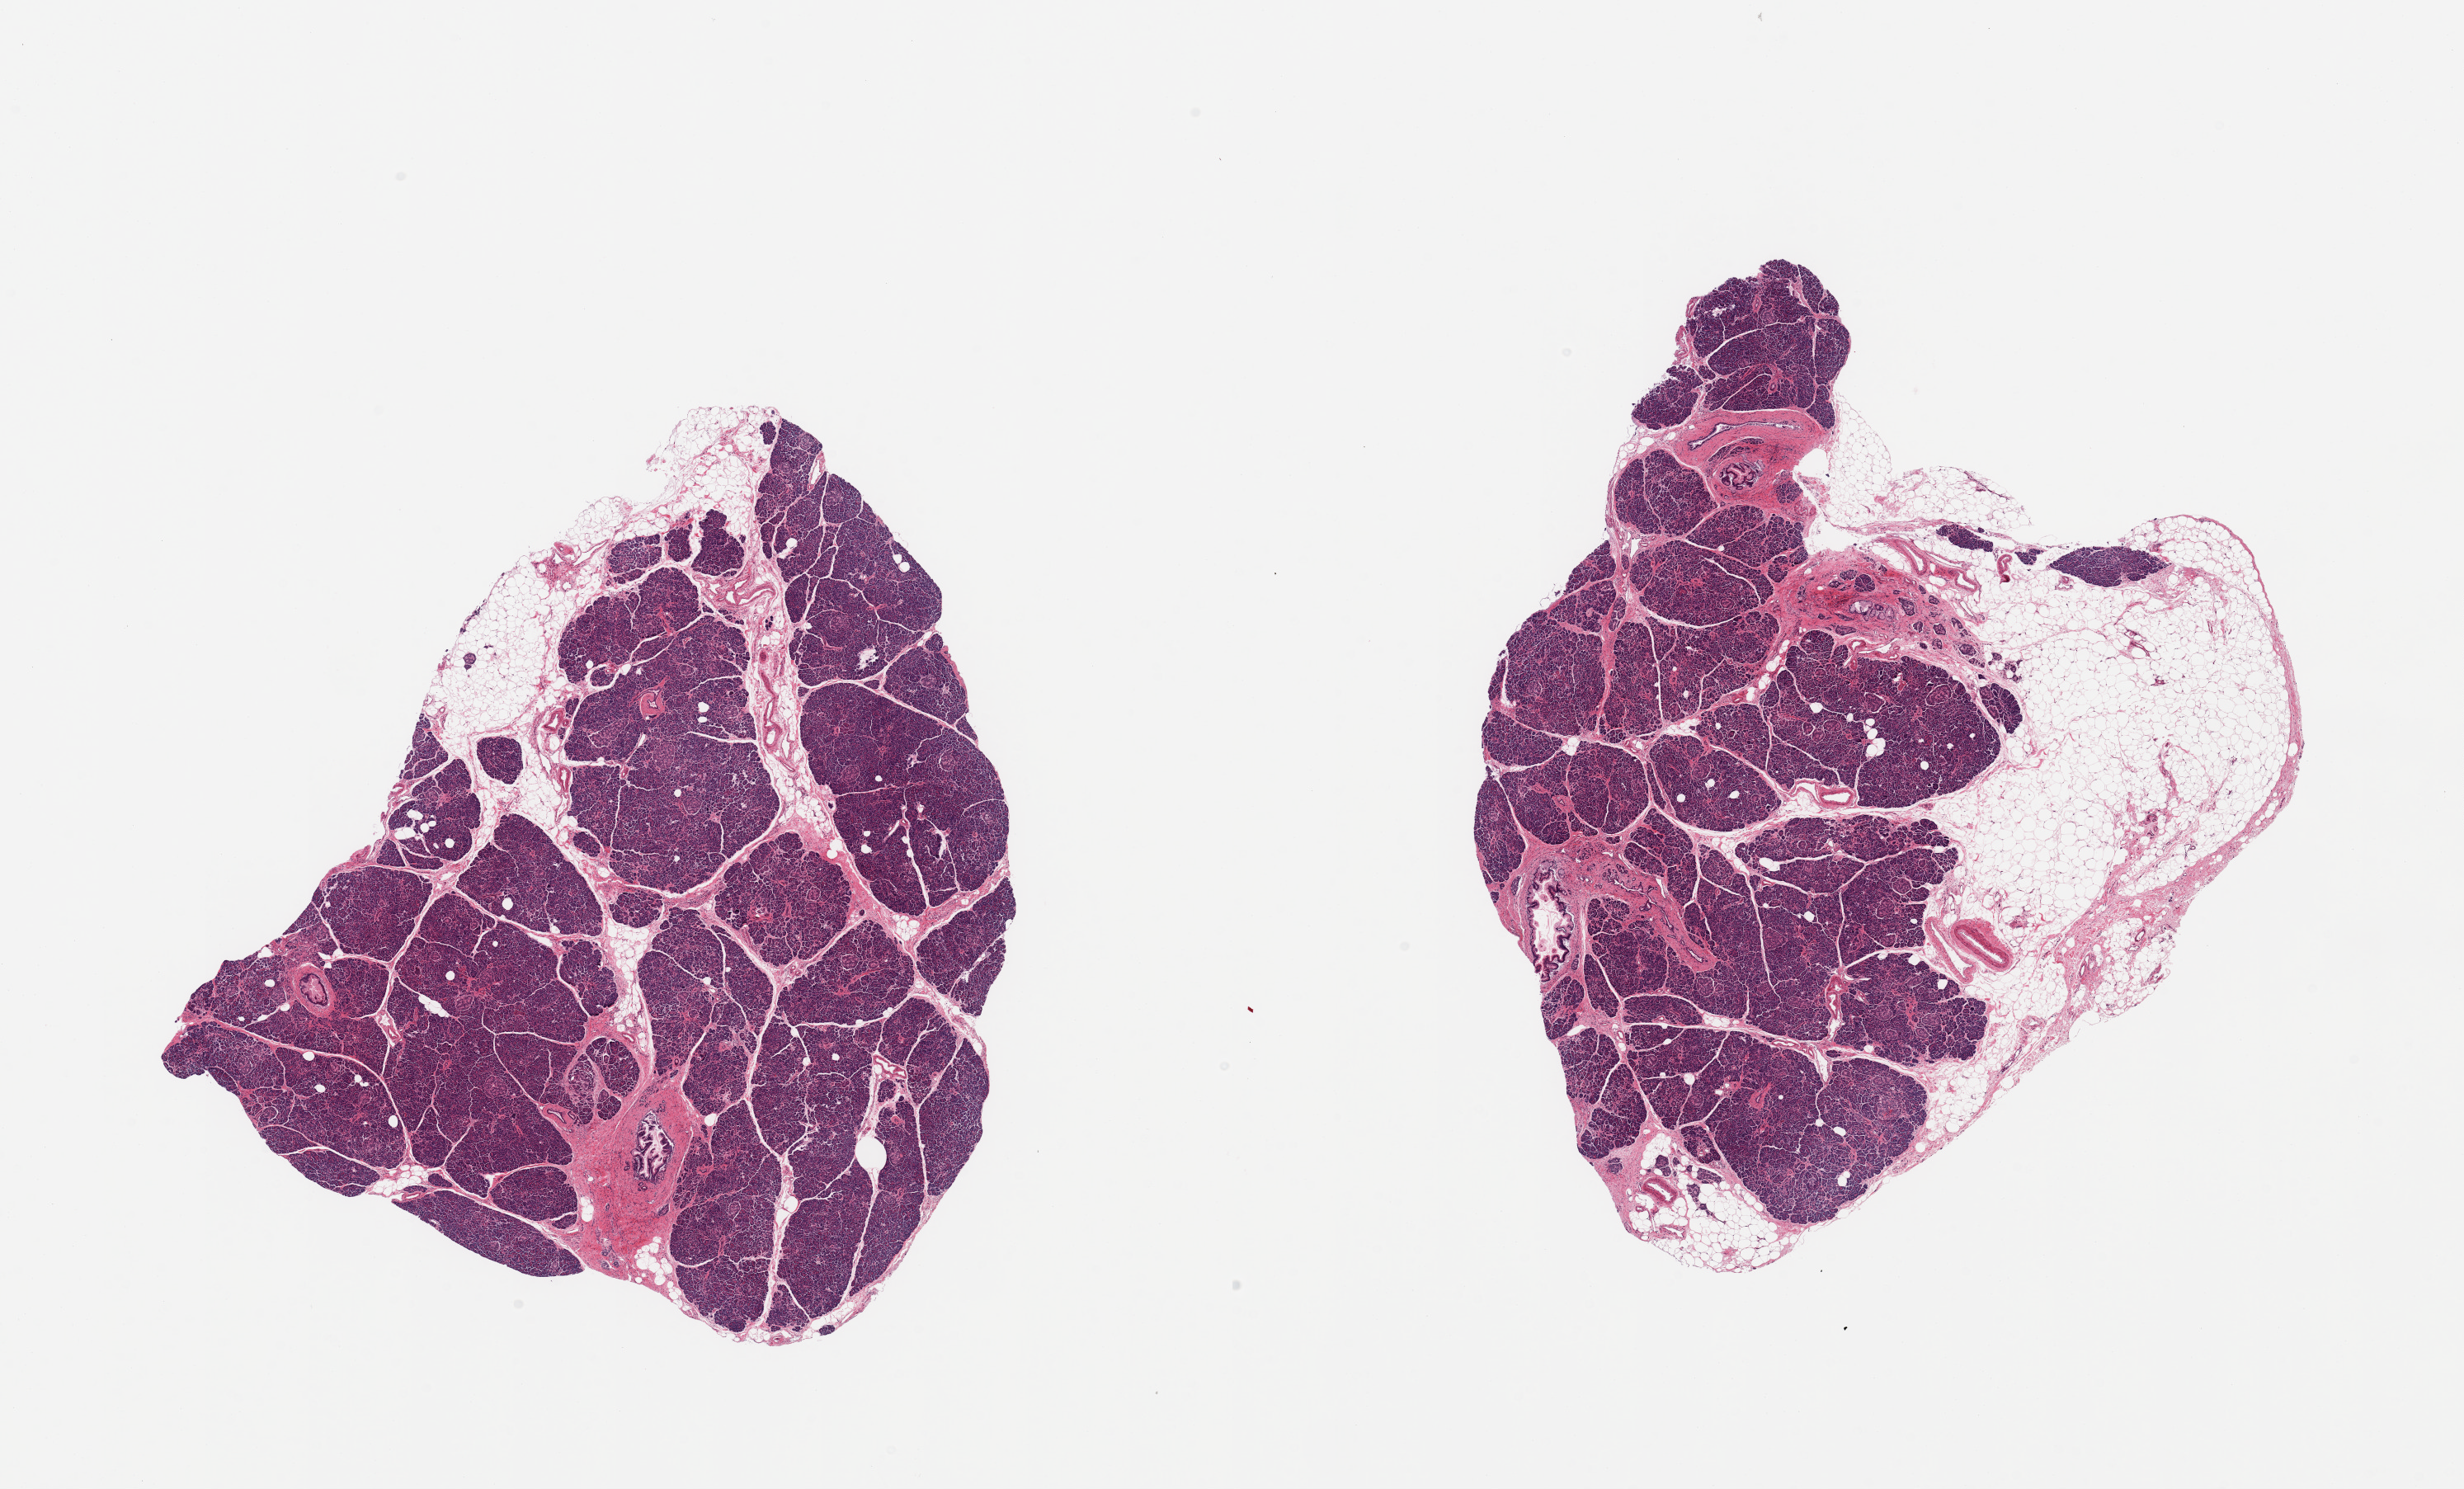
Haematoxylin and eosin whole-slide image, shown as a low-resolution overview of the whole scanned area (about 23.6 x 14.3 mm), PAXgene-fixed, paraffin-embedded tissue, section of pancreas (target tissue), tissue donor sample. Female donor.
Pathologist's review note for this sample: 2 pieces; foci of acinar atrophy & fibrosis with PanIN-1A/B; excessive external fat up to 2.8 mm.